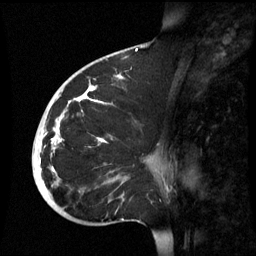
Breast MRI (dynamic contrast-enhanced), one sagittal slice. Slice 33 of 60 in the series (ordered by position). Dynamic contrast-enhanced series, image 2 of 3 at this slice position (ordered by acquisition). 1.5 T. TE 4.2 ms, TR 8.9 ms. 2.6 mm slice thickness. 256 × 256 image matrix, field of view 220 × 220 mm. Patient: female, 35 years. From the clinical record (not read from this slice): setting: breast cancer imaged before/during neoadjuvant chemotherapy; receptor status: HR-positive, HER2-negative.
Outlined on this slice (semi-automatic segmentation, software-assisted and operator-edited):
- analysis volume of interest (the breast-tissue region the enhancement analysis was run in; not a lesion): bounding box [x1, y1, x2, y2] px = [32, 74, 164, 221]
- tumour enhancement mask (voxels above the 70 % enhancement threshold inside the analysis volume of interest): [39, 76, 122, 173]